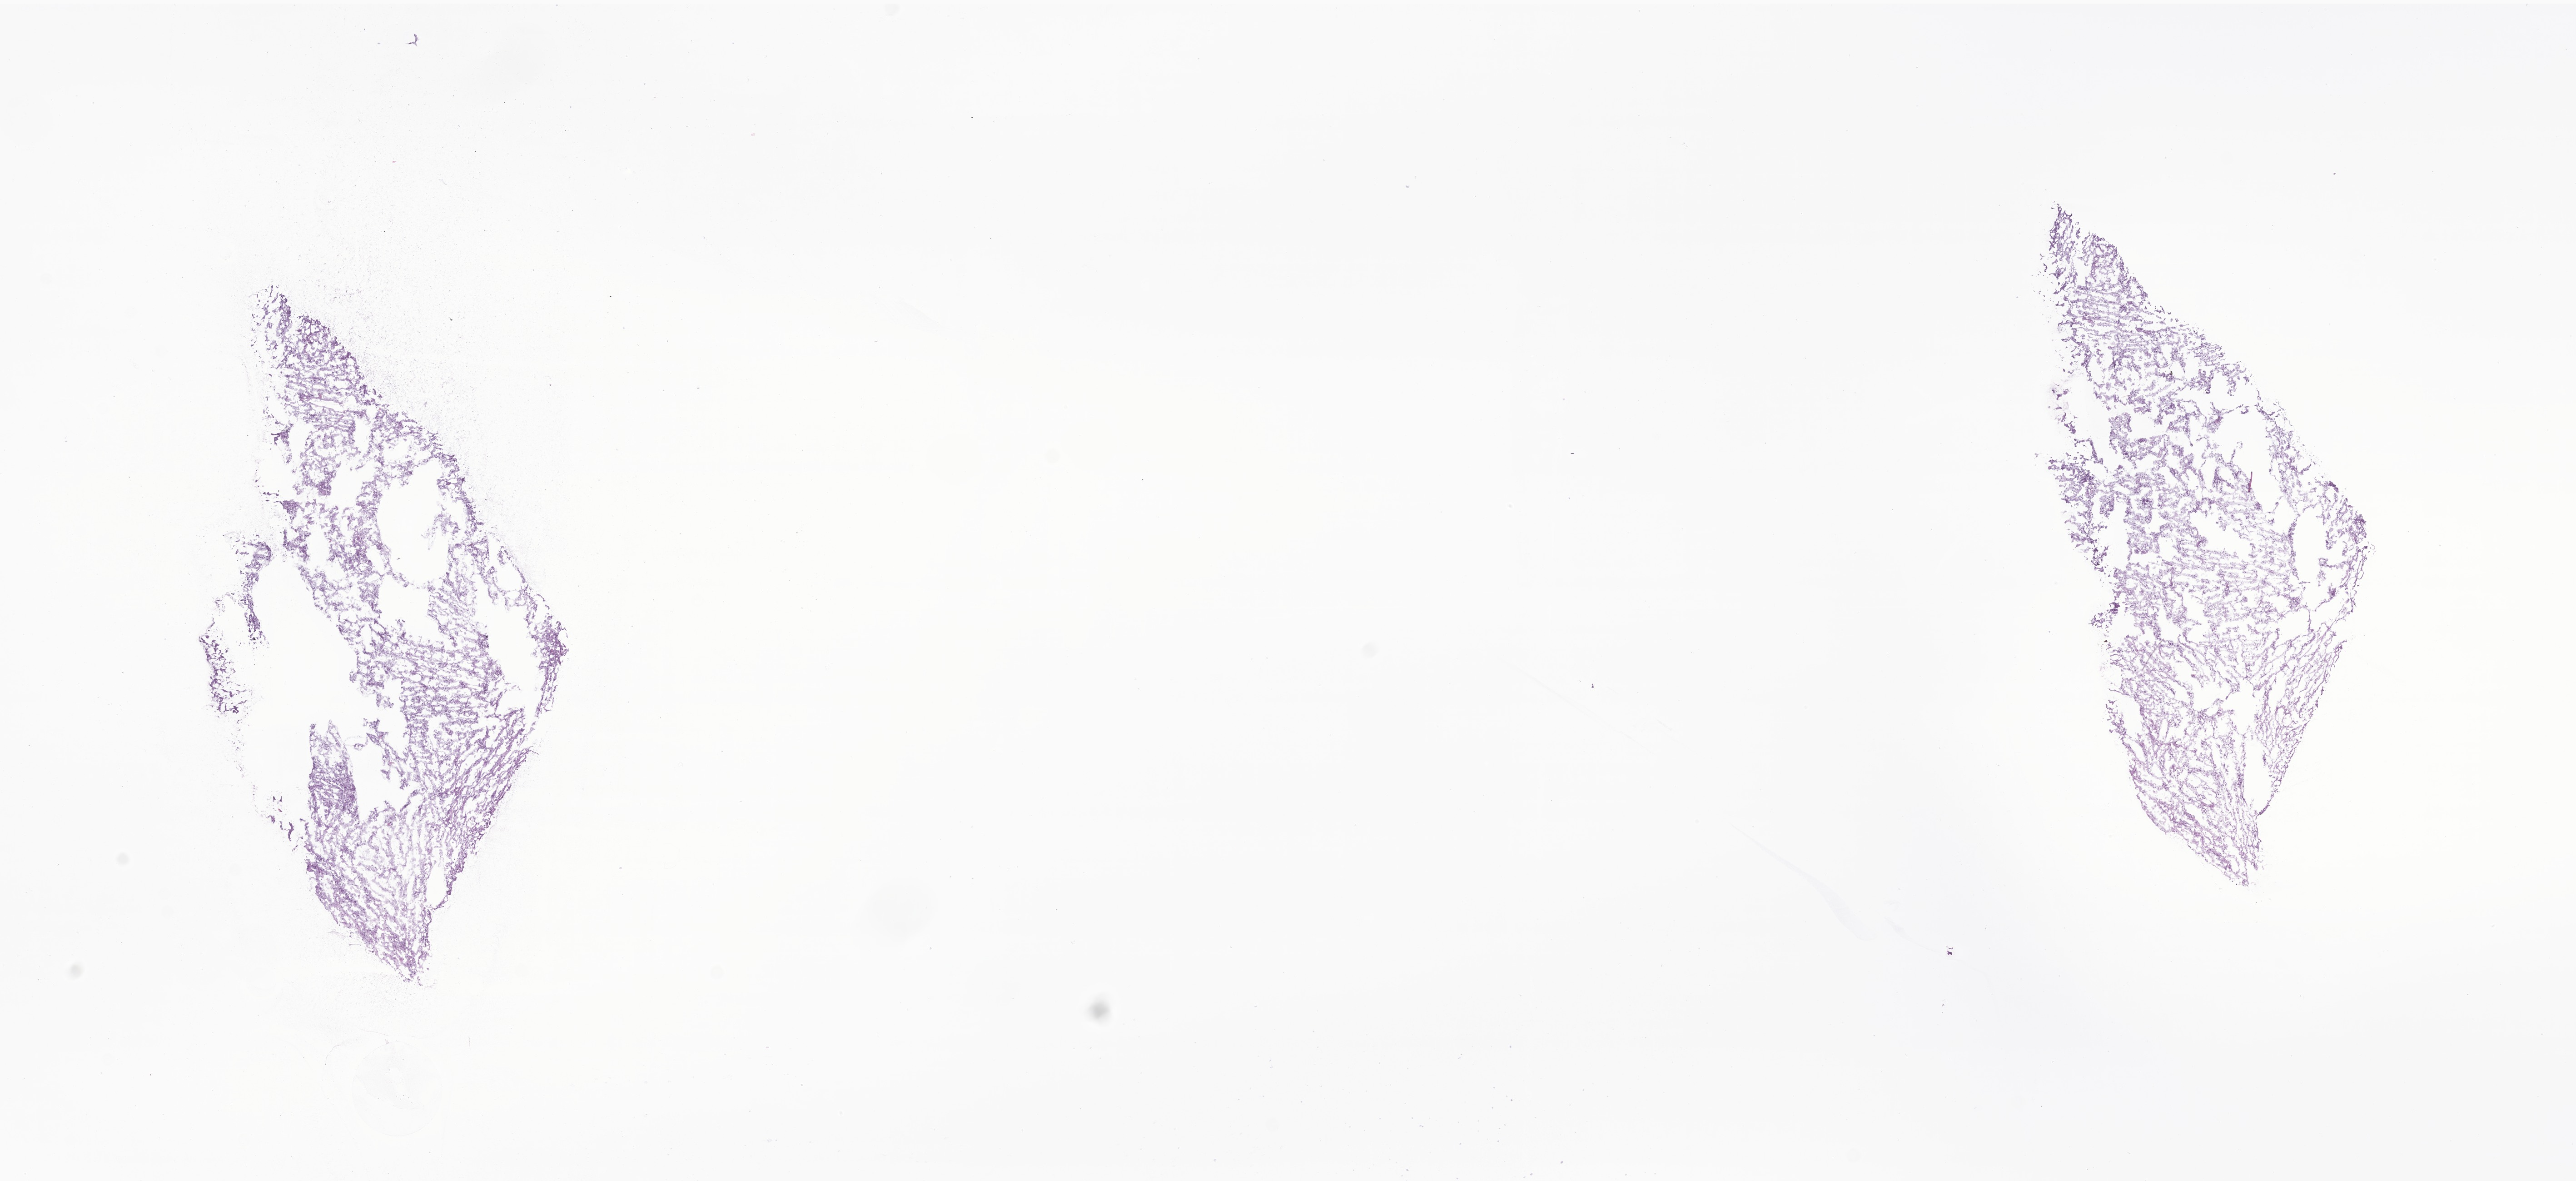
Hematoxylin and eosin (H&E) whole-slide image of tumor tissue from the temporal lobe, shown as a low-resolution overview of the whole scanned area (about 23.9 x 11.0 mm). Frozen section (OCT-embedded). Patient: male, age 161 months.
Diagnosis (ICD-O-3 morphology term): Ganglioglioma, NOS.